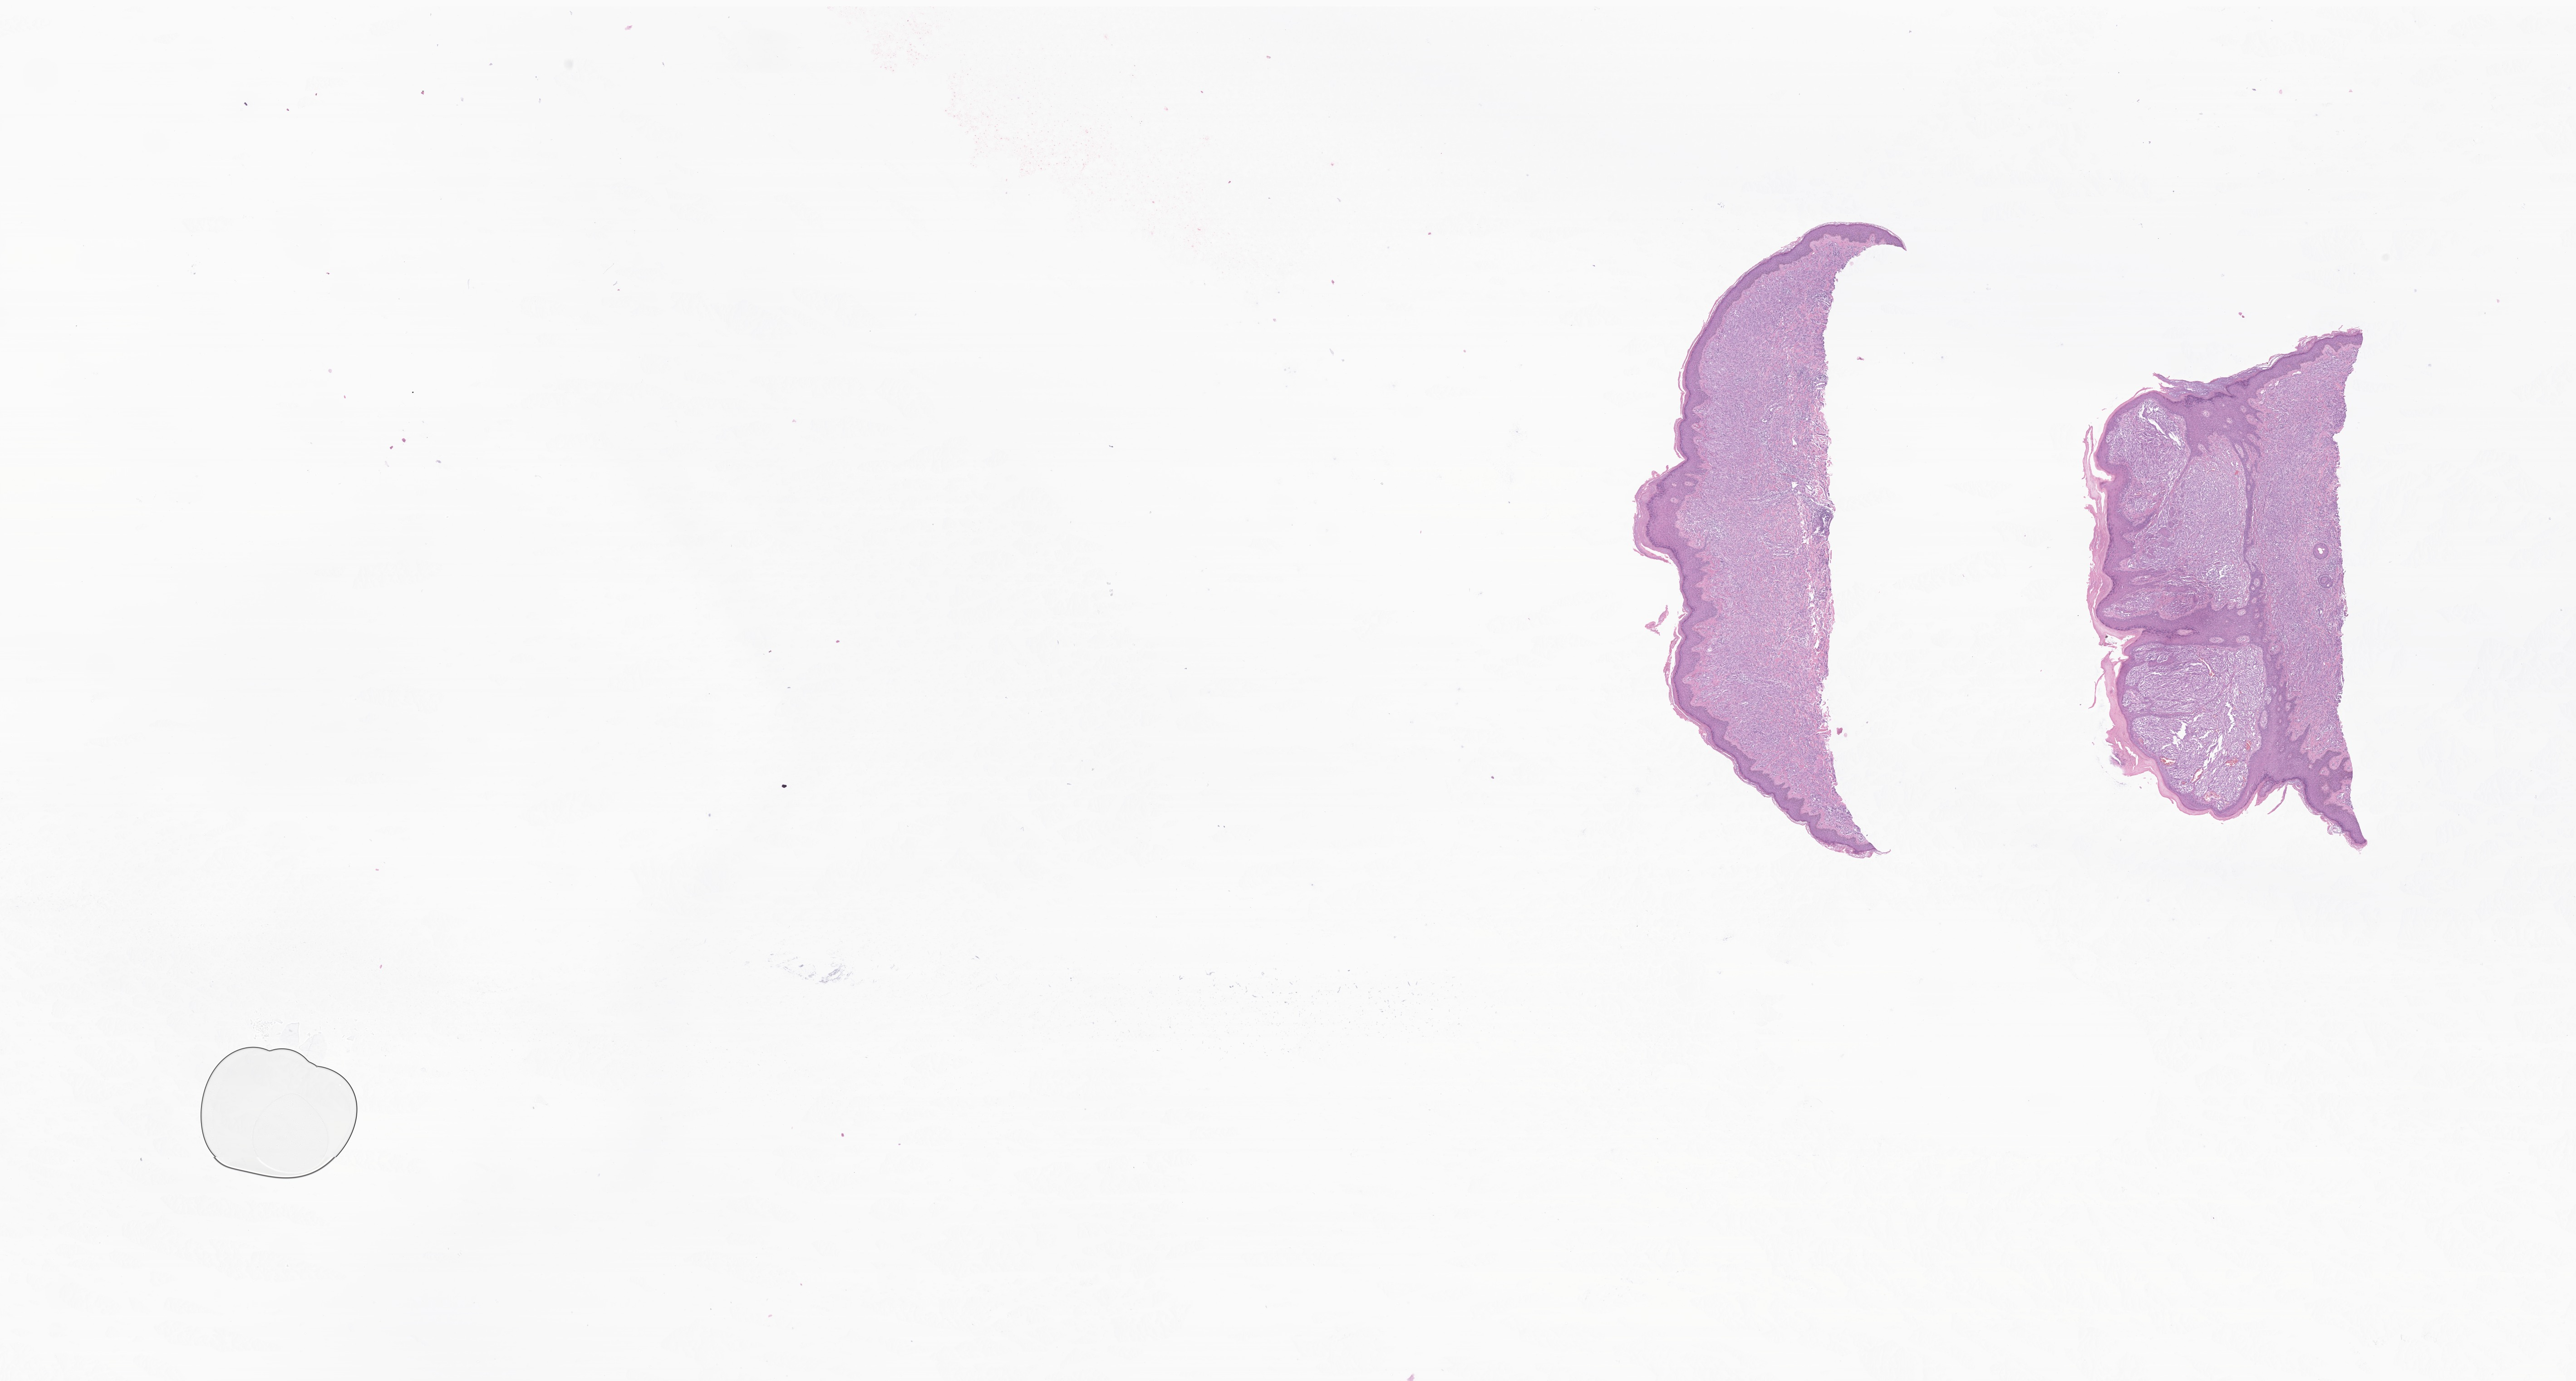
Digitized haematoxylin and eosin-stained section of tumor tissue from the skin of lower limb — a low-resolution overview of the entire scanned area, about 23.9 x 12.8 mm; formalin-fixed, paraffin-embedded (FFPE) tissue. Male patient, age 140 months (11 years 8 months).
Diagnosis (ICD-O-3 morphology term): Pigmented nevus, NOS.